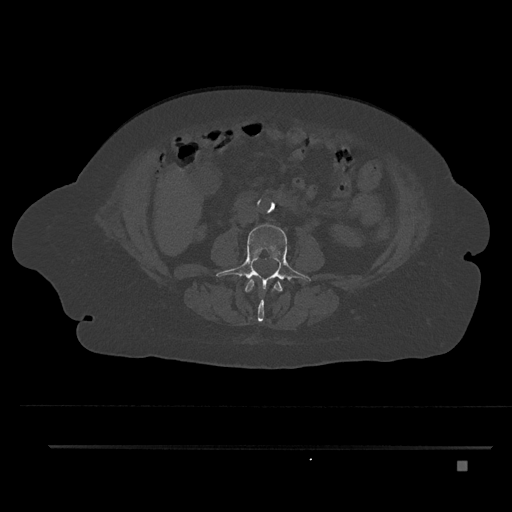
CT including the spine, one axial slice. Reconstruction kernel Br40s/3. 120 kVp. Bone window (W 1800 / L 400 HU). 0.5 mm slice thickness. 512 × 512 image matrix. Patient: female, 76 years. Case-level facts recorded for this patient, not image findings: primary cancer: lung; vertebrae with lytic lesions (as recorded): T11, L3.
Outlined on this slice (semi-automatically segmented with operator editing):
- L2 vertebra: box from (x=245, y=279) to (x=283, y=322) px
- L3 vertebra: (x=216, y=224)–(x=311, y=290)